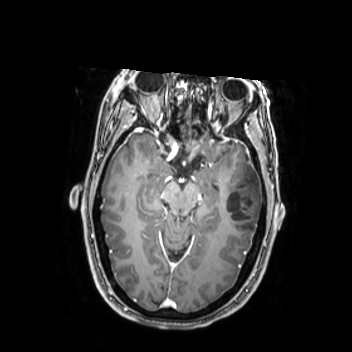
Brain MRI from a brain-tumour surgery series, one axial slice. Slice 159 of 350 in the series (ordered by position). T1-weighted post-contrast. 352 × 352 image matrix. From the clinical record (not read from this slice): histopathology: Oligodendroglioma; WHO grade: 2; IDH mutation: yes.
Annotated regions visible in this slice (manually delineated by an expert):
- tumour: bounding box <224,163,262,236> (left, top, right, bottom; pixels)